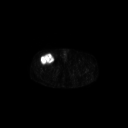
FDG PET of an extremity soft-tissue mass (from a PET/CT study), one axial slice; position 299 of 311 along the scan axis; 128 × 128 image matrix, field of view 700 × 700 mm. Male patient, age 56 years. From the clinical record (not read from this slice): histological type: pleiomorphic leiomyosarcoma; grade: intermediate; site of the primary tumour: right thigh.
Structures marked on this image (expert contour drawn on MRI and transferred to this co-registered scan by the dataset authors):
- gross tumour volume including surrounding oedema: bounding box (x1, y1, x2, y2) in pixels: (40, 53, 54, 65)
- gross tumour volume (mass): (41, 53, 54, 65)